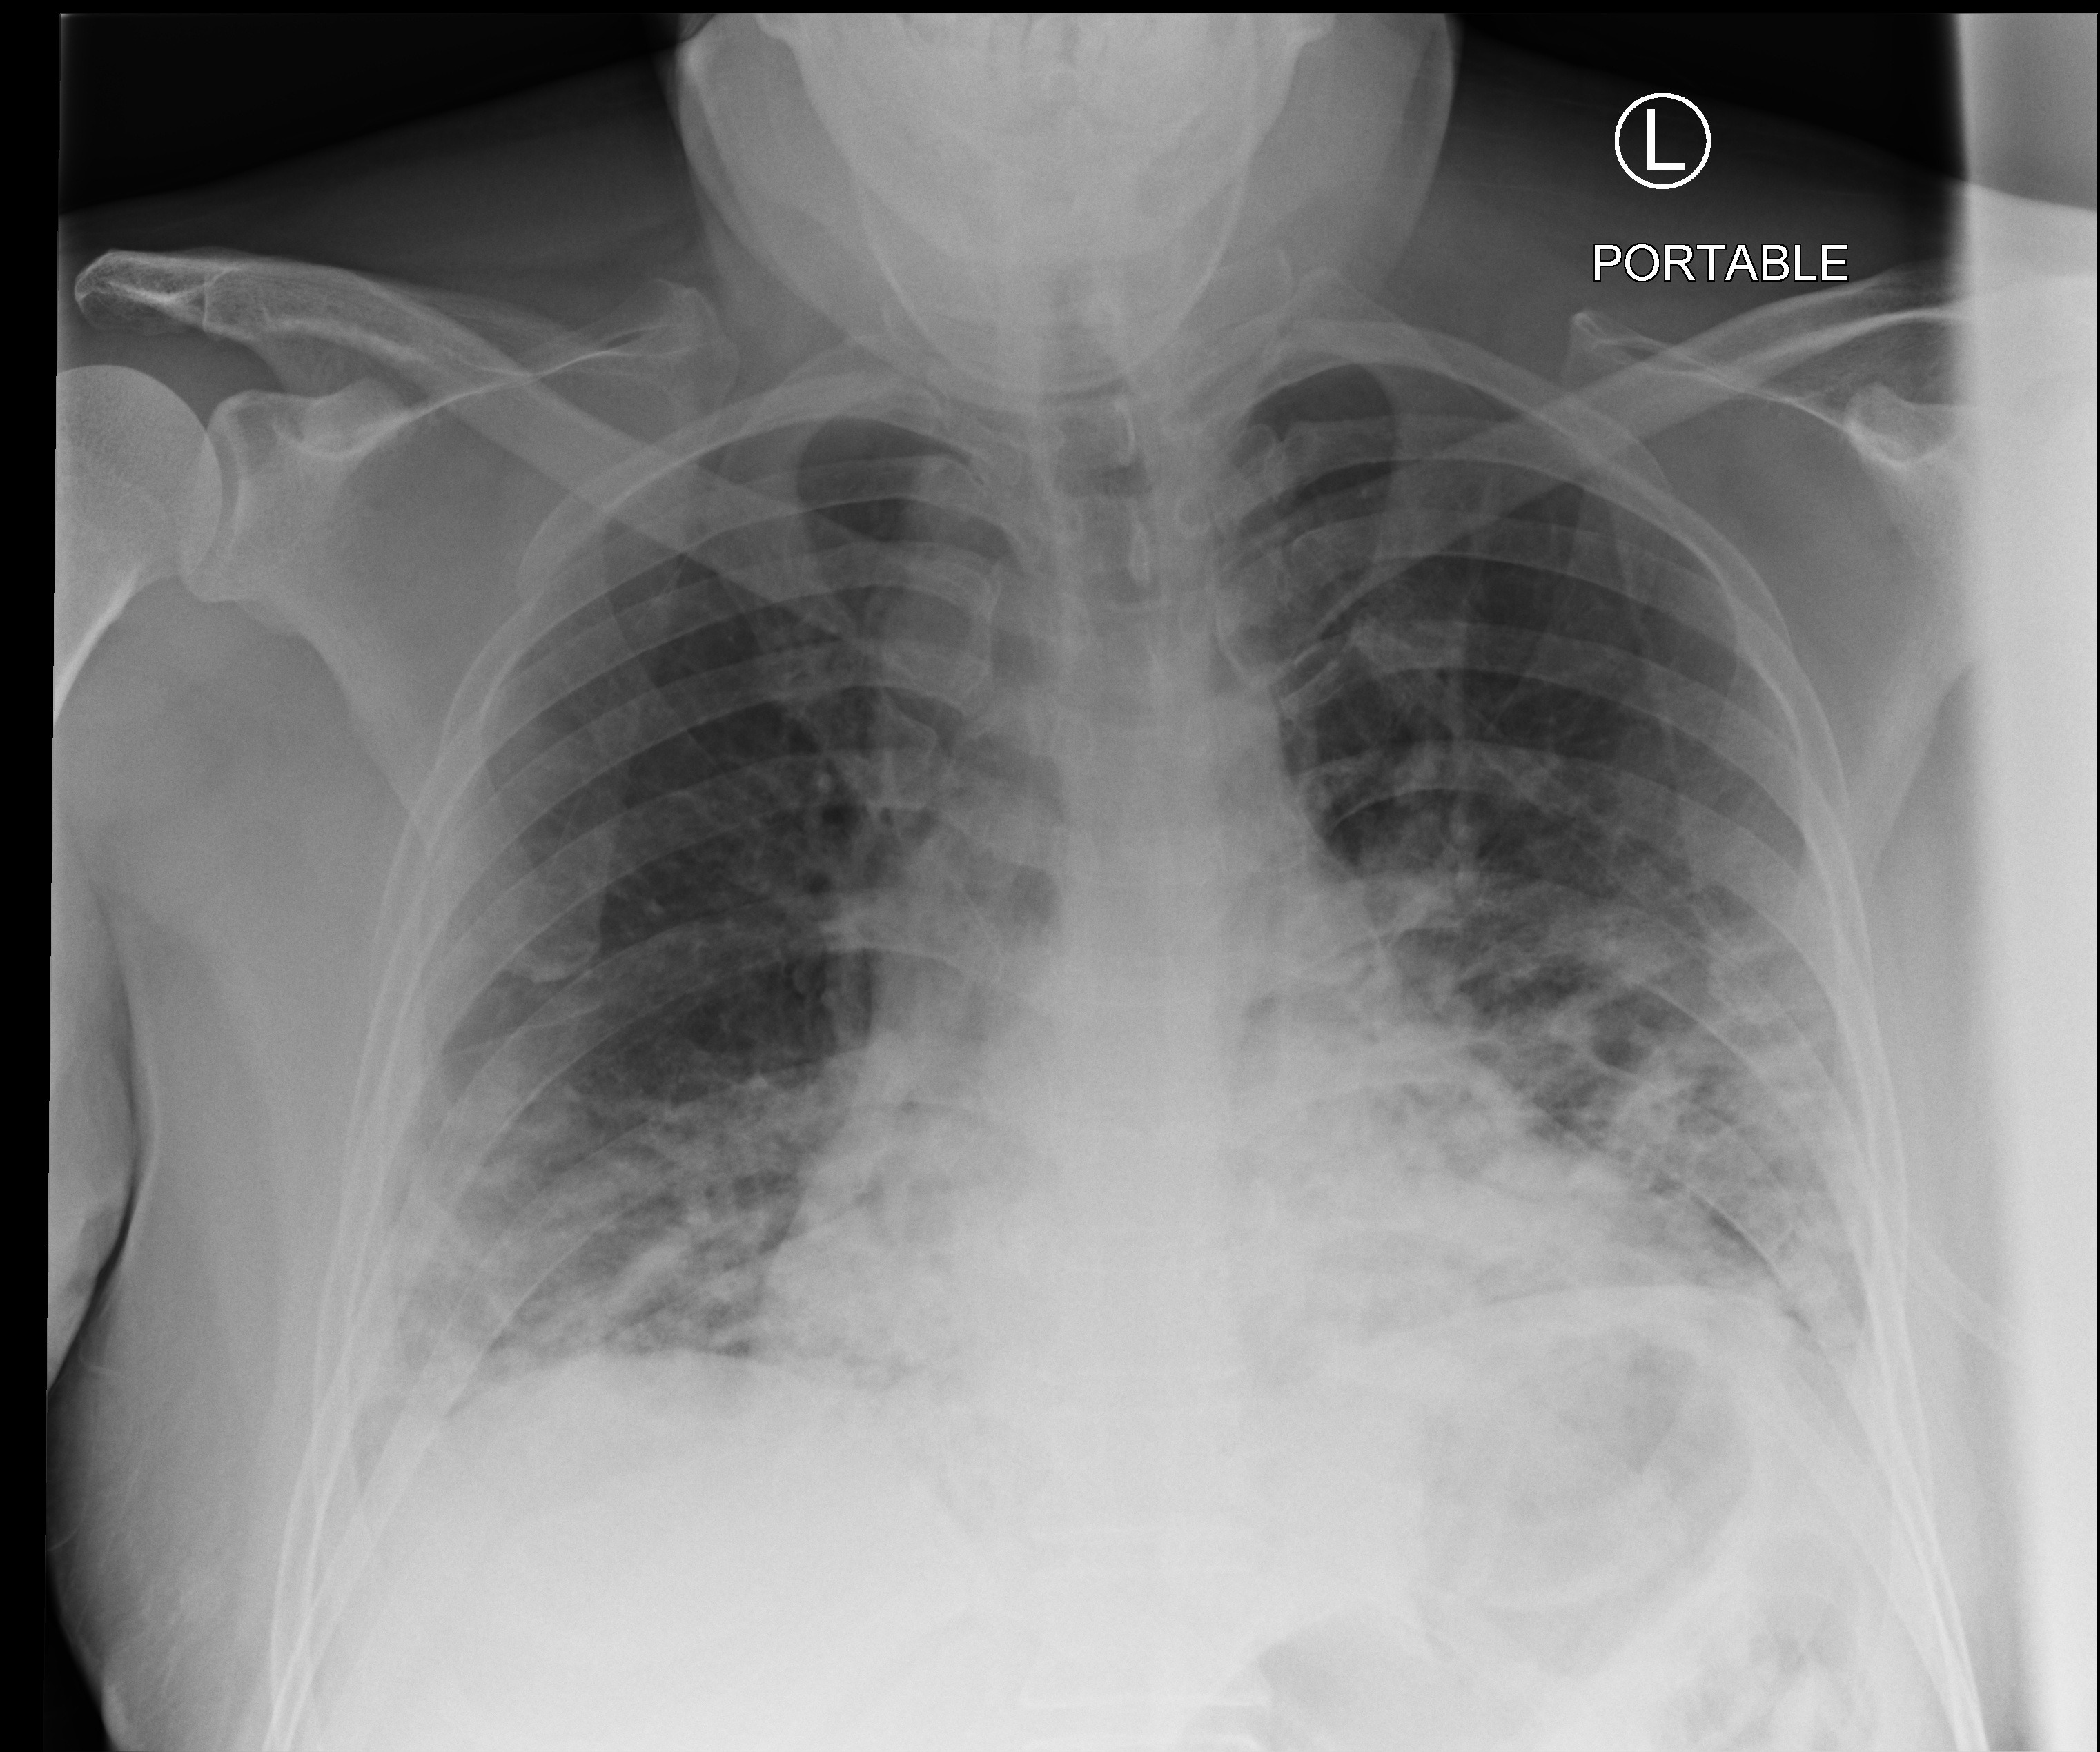
Chest X-ray (portable), anteroposterior (AP) projection. Male patient hospitalised with COVID-19, age 18–59 years.
From the hospital-stay record, not from the radiograph (when in the stay this image was taken is not recorded):
- mechanically ventilated during this hospital stay: yes
- admitted to intensive care during this hospital stay: yes